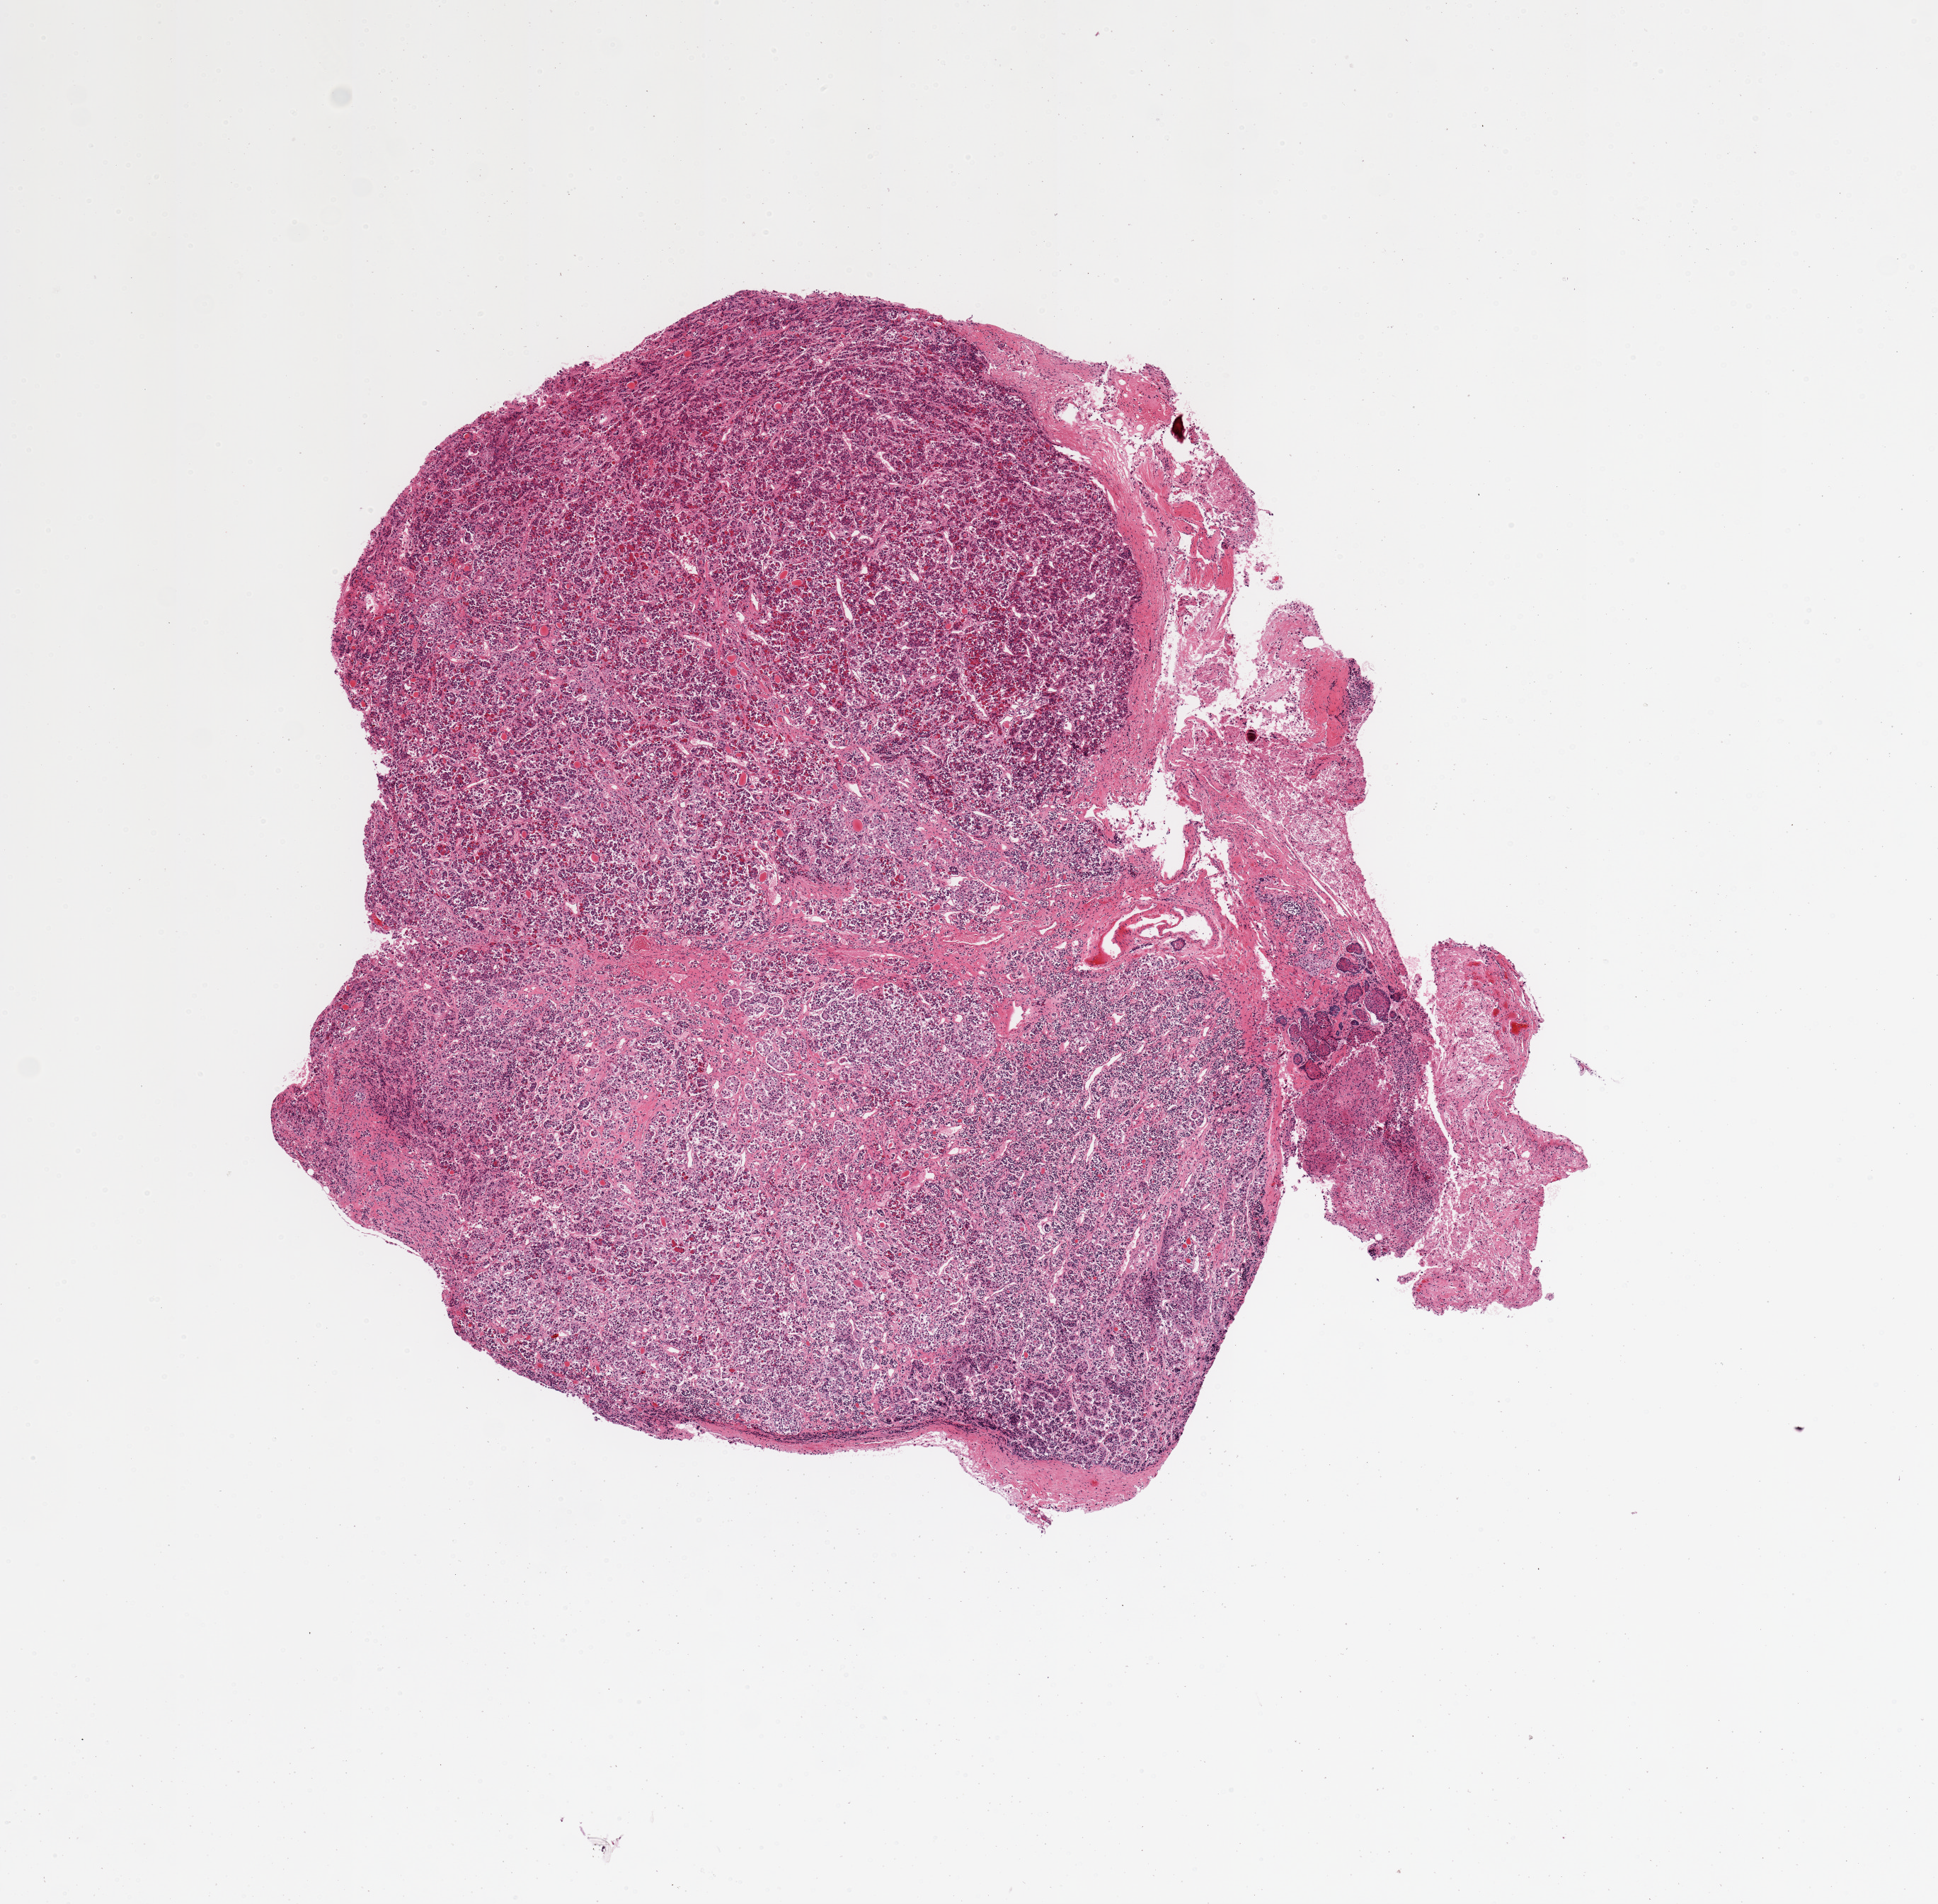
Haematoxylin and eosin whole-slide image, brightfield — whole scanned area (about 10.8 x 10.6 mm, acquisition: 20x scan) shown as a low-resolution overview, PAXgene-fixed, paraffin-embedded tissue, sampled site (target tissue): pituitary, donor tissue sample. Donor: male.
Reviewer comment on this tissue sample: 1 piece, trace neurohypophysis; largley adenohypophysis.